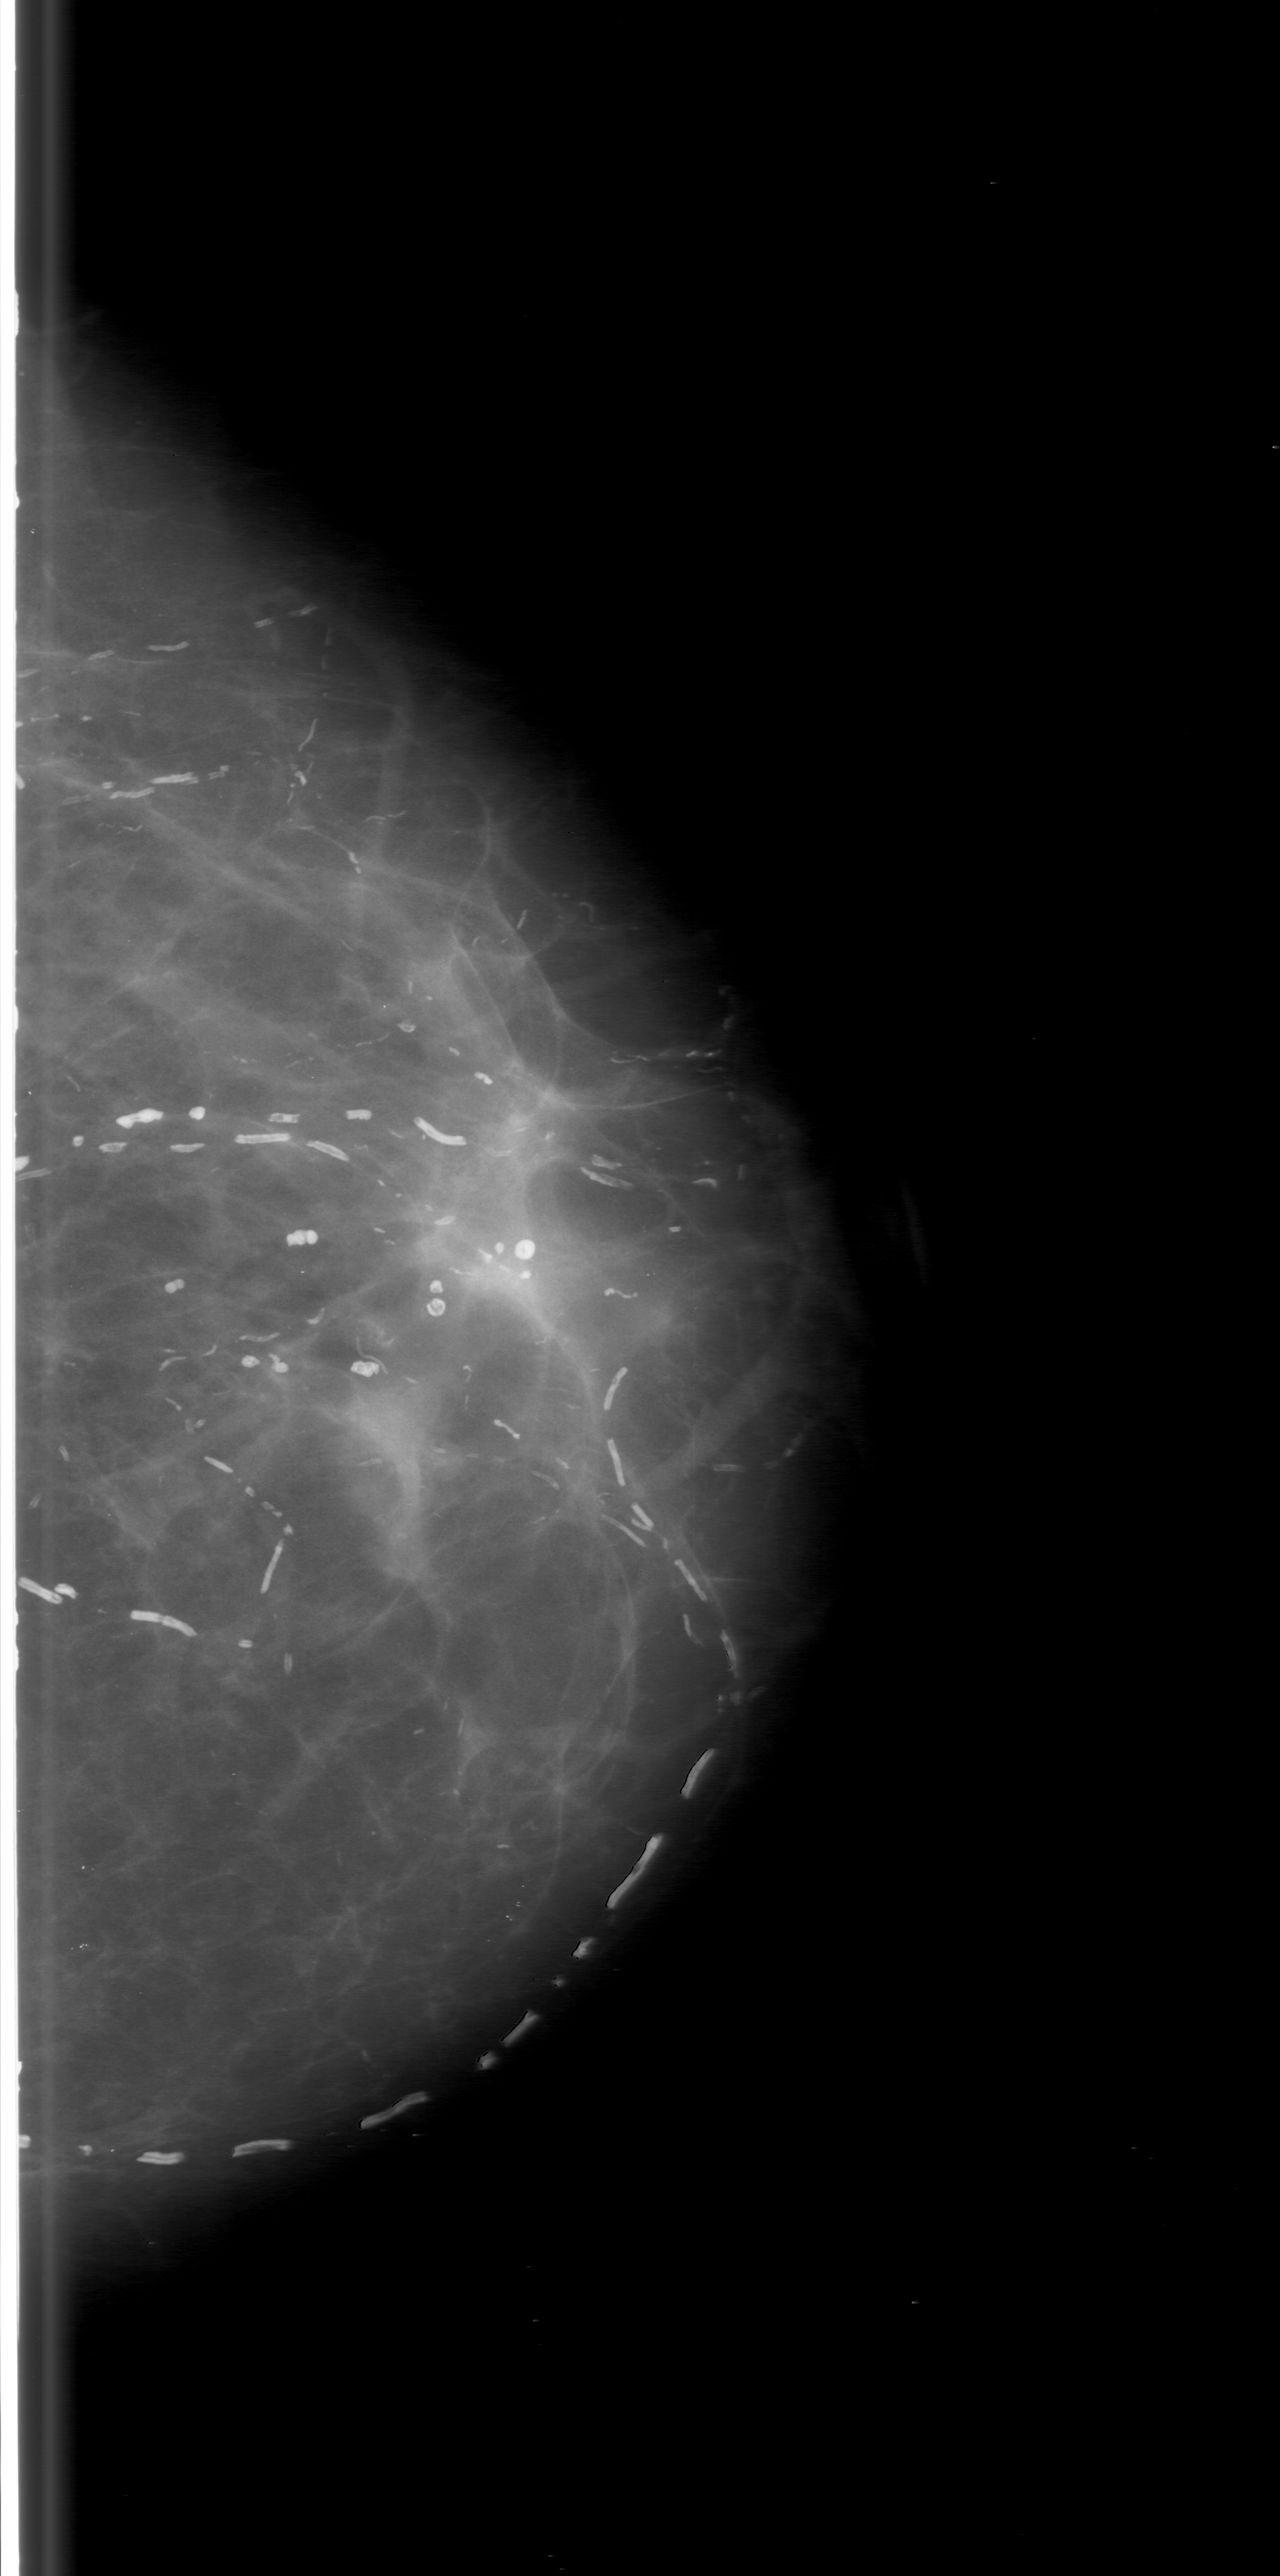
Digitized screen-film mammogram, left breast, craniocaudal (CC) view, breast composition: scattered fibroglandular densities (BI-RADS density category 2 of 4).
Marked abnormality: mass, shape irregular, margins ill defined; BI-RADS assessment category 3; subtlety rating 3 on a 1 (subtle) to 5 (obvious) scale; pathology (as recorded): malignant.